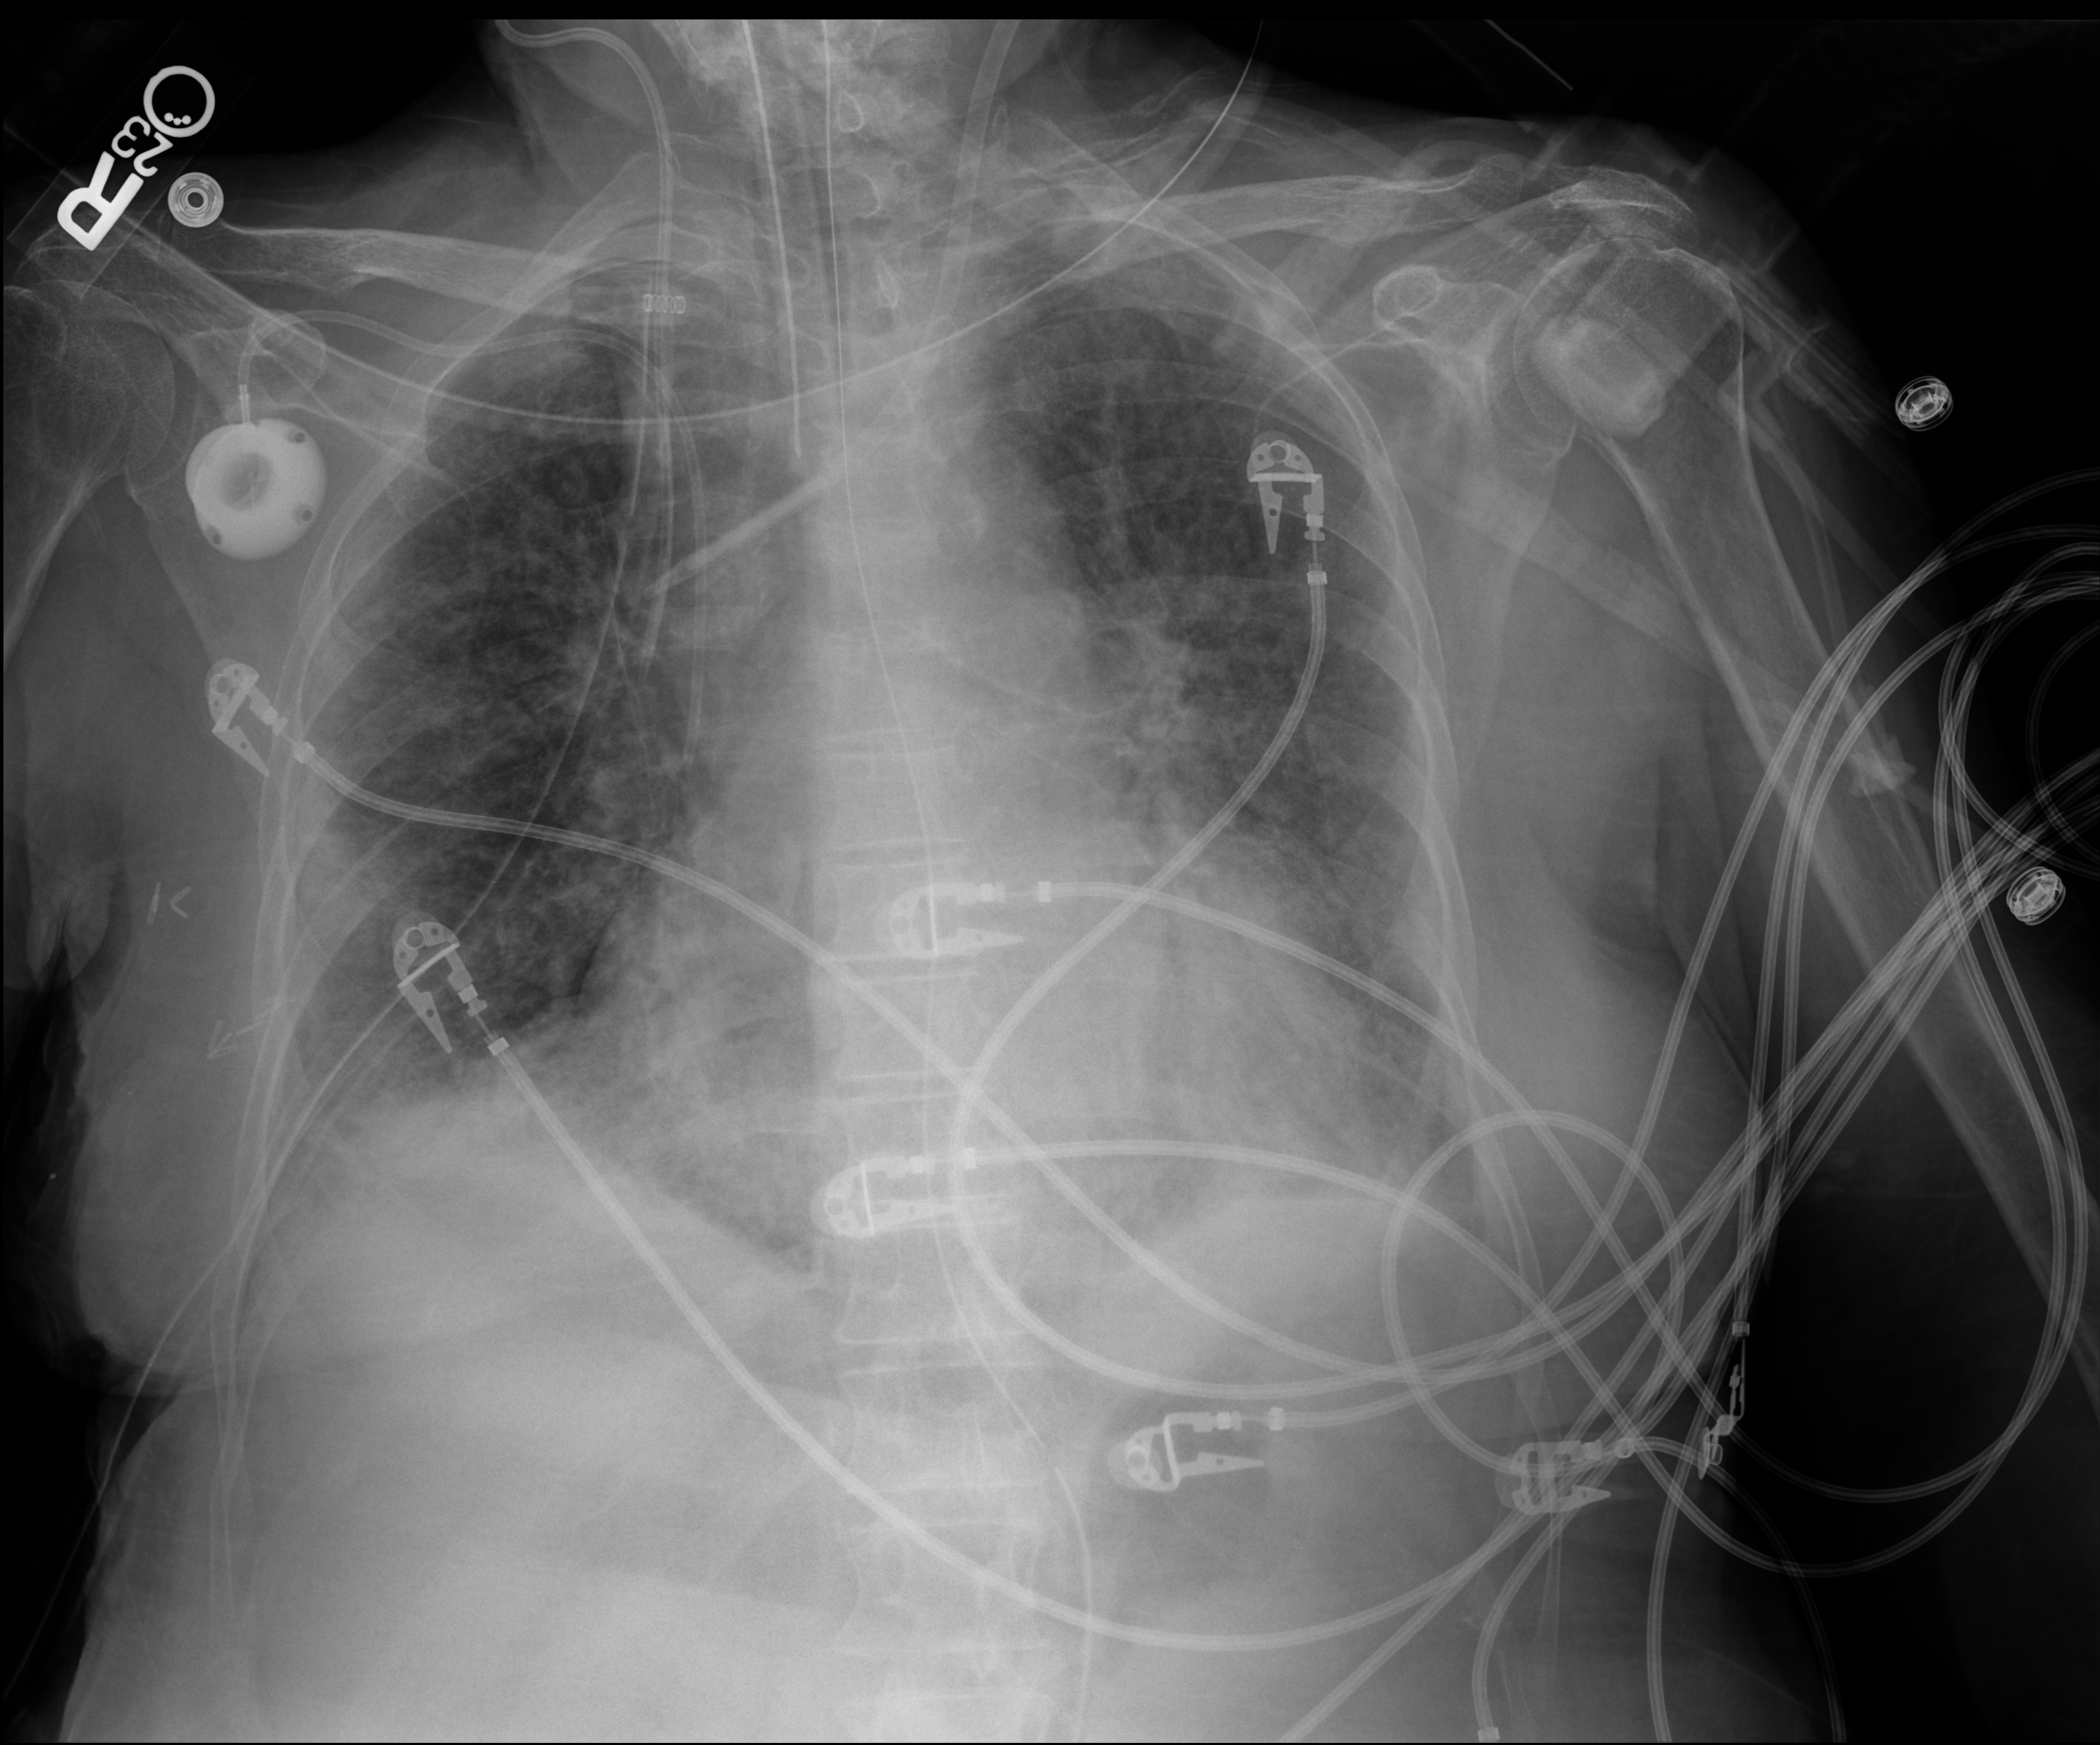
Chest X-ray (portable); anteroposterior (AP) projection. Patient hospitalised with COVID-19; female, aged 60–74 years.
Hospital-stay facts (about this admission, not read from this image; timing relative to this image not recorded): admitted to intensive care during this hospital stay: yes; mechanically ventilated during this hospital stay: yes.